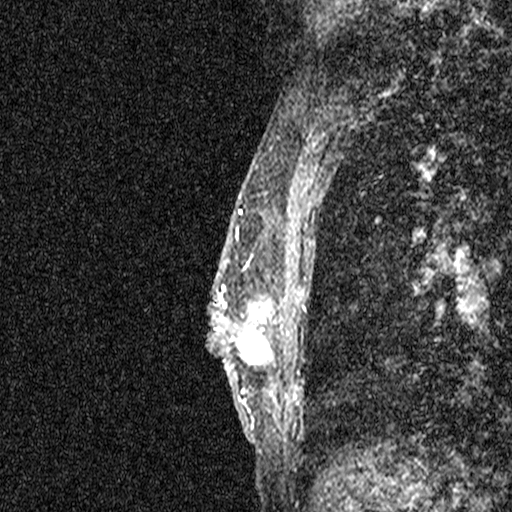
Breast MRI (dynamic contrast-enhanced), one sagittal slice. Position 22 of 44 along the scan axis. Dynamic contrast-enhanced study with each time point stored as its own series, time point 2 of 3 at this slice position (early post-contrast, ordered by acquisition time). 1.5 T. TE 4.5 ms, TR 11 ms. 2.05 mm slice thickness. 512 × 512 image matrix, field of view 200 × 200 mm. Patient: female, 44 years. From the clinical record (not read from this slice): setting: breast cancer imaged before/during neoadjuvant chemotherapy; receptor status: HR-positive, HER2-negative.
Annotated regions visible in this slice (semi-automatically segmented with operator editing):
- analysis volume of interest (the breast-tissue region the enhancement analysis was run in; not a lesion): bounding box <204,254,278,401> (left, top, right, bottom; pixels)
- tumour enhancement mask (voxels above the 90 % enhancement threshold inside the analysis volume of interest): <207,254,272,396>